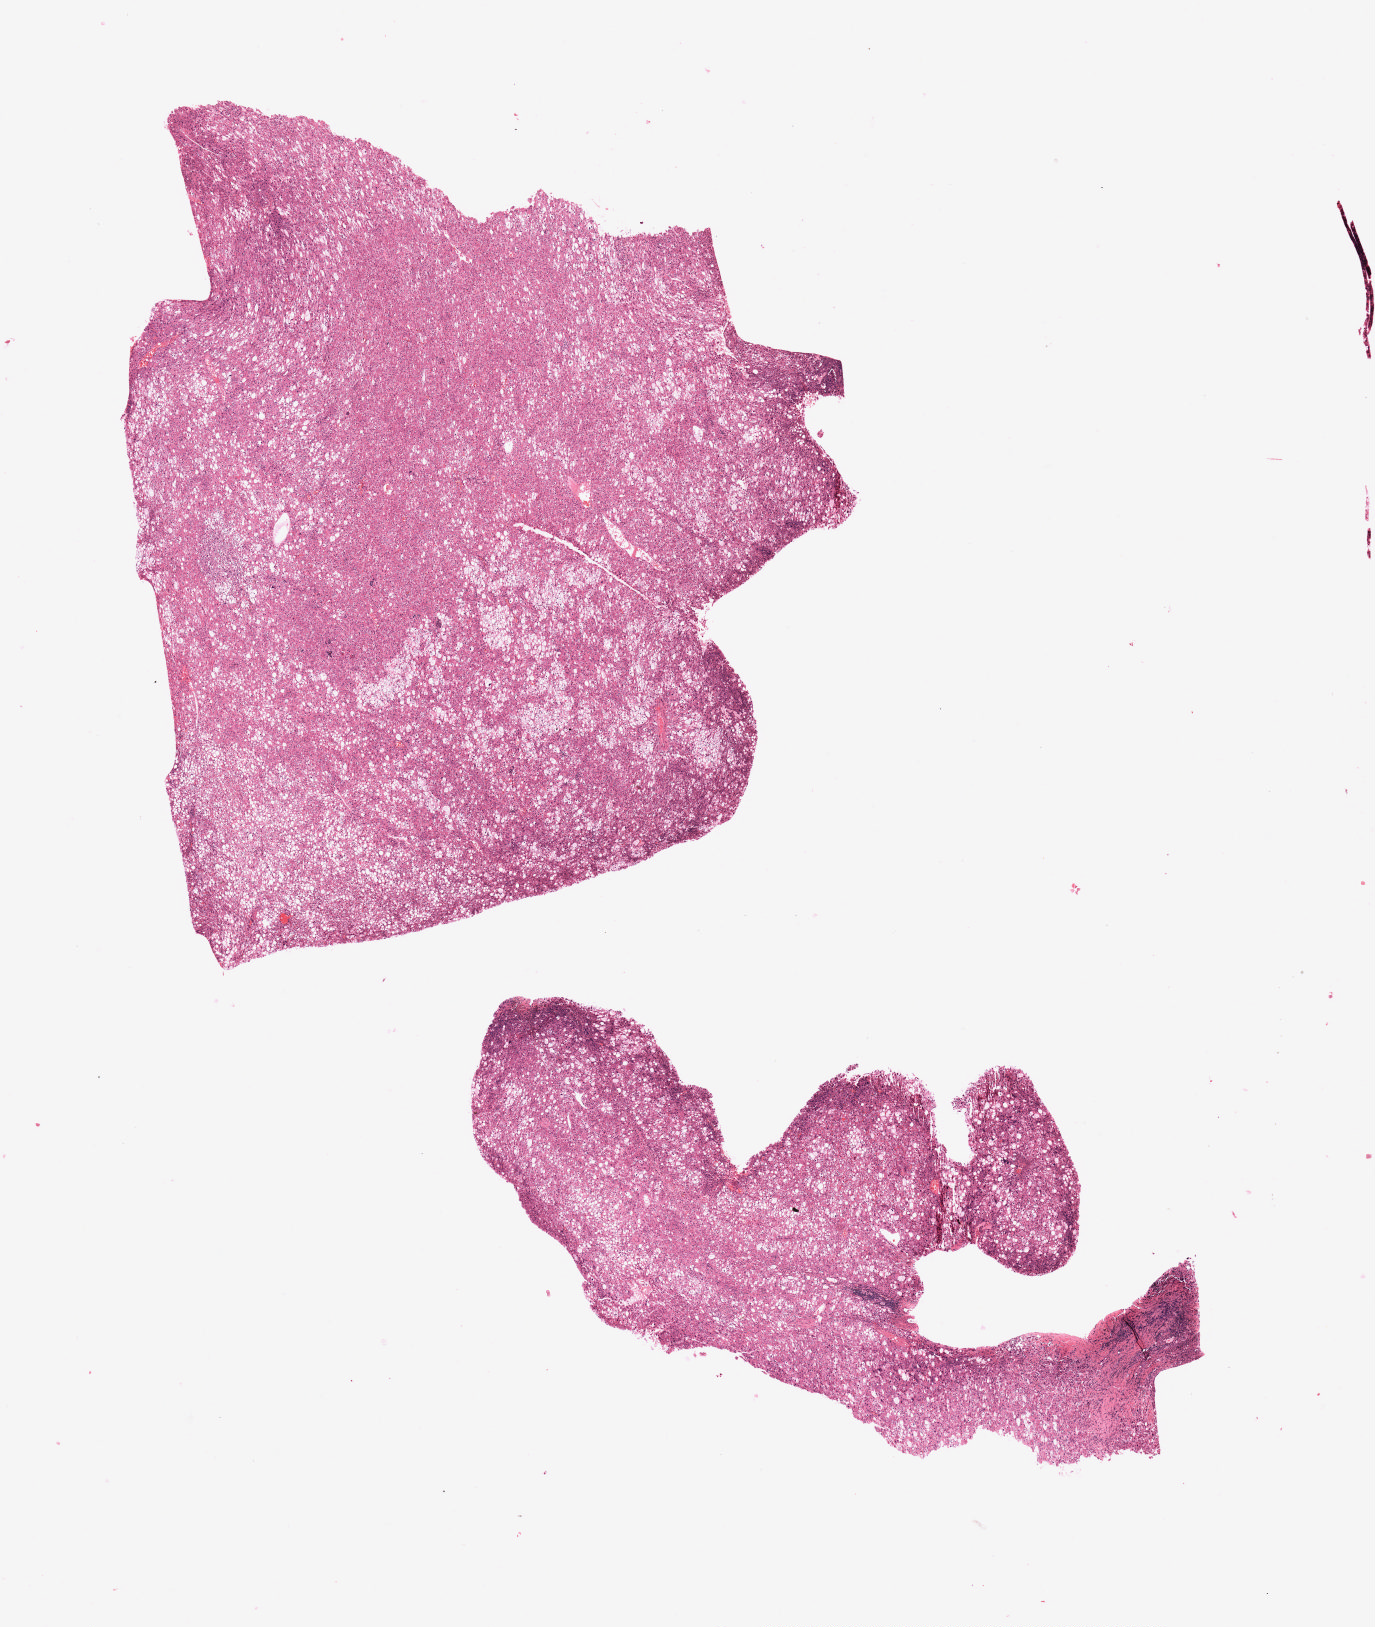
H&E whole-slide image — whole scanned area (about 11.0 x 13.0 mm) shown as a low-resolution overview; FFPE section; sample: primary tumour, liver. Male patient; age at initial diagnosis 58 years. Histologic grade: G1 (well differentiated).
- AJCC pathologic stage: I
- histologic diagnosis: Hepatocellular carcinoma, NOS